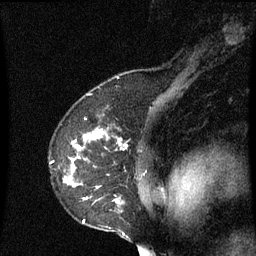
Breast MRI (dynamic contrast-enhanced), one sagittal slice. Slice 48 of 60 in the series (ordered by position). Dynamic contrast-enhanced series, image 2 of 3 at this slice position (ordered by acquisition). 1.5 T. TE 4.2 ms, TR 8.9 ms. 2 mm slice thickness. 256 × 256 image matrix, field of view 200 × 200 mm. Female patient, age 53 years. From the clinical record (not read from this slice): setting: breast cancer imaged before/during neoadjuvant chemotherapy; receptor status: HR-positive, HER2-negative.
Outlined on this slice (semi-automatically segmented with operator editing):
- analysis volume of interest (the breast-tissue region the enhancement analysis was run in; not a lesion): bounding box [x1, y1, x2, y2] px = [52, 130, 157, 231]
- tumour enhancement mask (voxels above the 70 % enhancement threshold inside the analysis volume of interest): [66, 130, 127, 223]